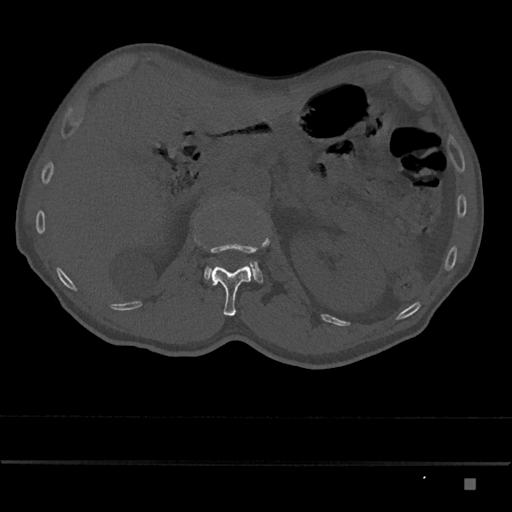
CT including the spine, one axial slice; slice 525 of 797 in the series (ordered by position); bone window (W 1800 / L 400 HU); 0.5 mm slice thickness; 512 × 512 image matrix, field of view 390 × 390 mm. Male patient, age 72 years. From the clinical record (not read from this slice): primary cancer: prostate.
Outlined on this slice (semi-automatic segmentation, software-assisted and operator-edited):
- L1 vertebra: bounding box [x1, y1, x2, y2] px = [205, 237, 270, 316]
- L2 vertebra: [204, 262, 263, 283]